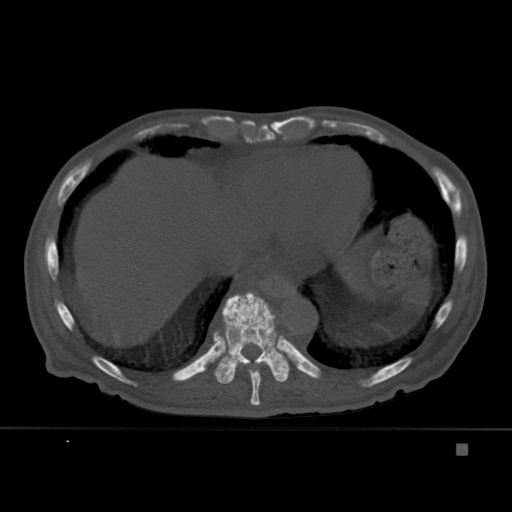
CT including the spine, one axial slice. Slice 237 of 451 in the series (ordered by position). Bone window (W 1800 / L 400 HU). 512 × 512 image matrix, field of view 378 × 378 mm. Patient: male, 75 years. Case-level facts recorded for this patient, not image findings: primary cancer: prostate.
Structures marked on this image (semi-automatic segmentation, software-assisted and operator-edited):
- T10 vertebra: box from (x=213, y=292) to (x=290, y=384) px
- T9 vertebra: (x=235, y=363)–(x=266, y=405)